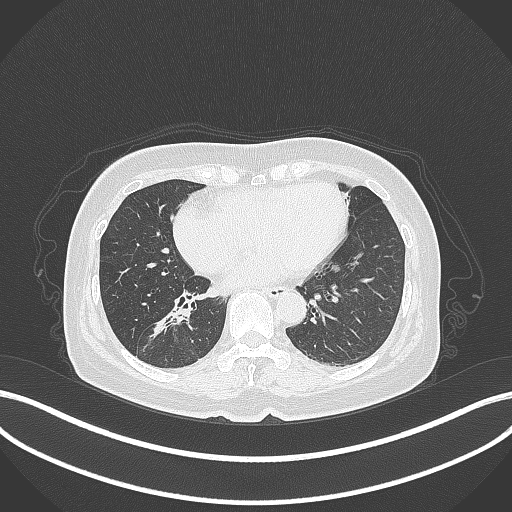
Chest CT, one axial slice; slice 154 of 429 in the series (ordered by position); reconstruction kernel B70f; 120 kVp; lung window (W 1500 / L -600 HU); 1 mm slice thickness; 512 × 512 image matrix. Female patient, age 67 years. Case-level facts recorded for this patient, not image findings: clinical TNM (as recorded): T1c N1 M0; histopathological grade: G2-3.
Outlined on this slice (bounding box drawn by a radiologist):
- lung tumour (recorded histology: adenocarcinoma): bounding box <146,301,194,352> (left, top, right, bottom; pixels)